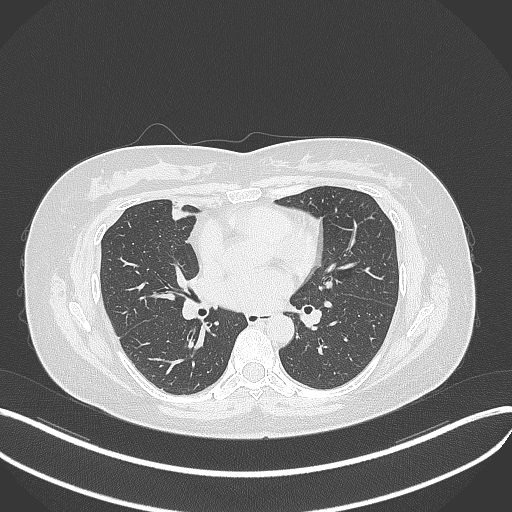
Chest CT, one axial slice; position 155 of 273 along the scan axis; lung window (W 1500 / L -600 HU); 1 mm slice thickness; 512 × 512 image matrix, field of view 400 × 400 mm. Female patient, age 42 years. Case-level facts recorded for this patient, not image findings: clinical TNM (as recorded): T1b N0 M0.
Outlined on this slice (rectangle marked by the reading radiologist):
- lung tumour (recorded histology: adenocarcinoma): bounding box <165,203,192,225> (left, top, right, bottom; pixels)